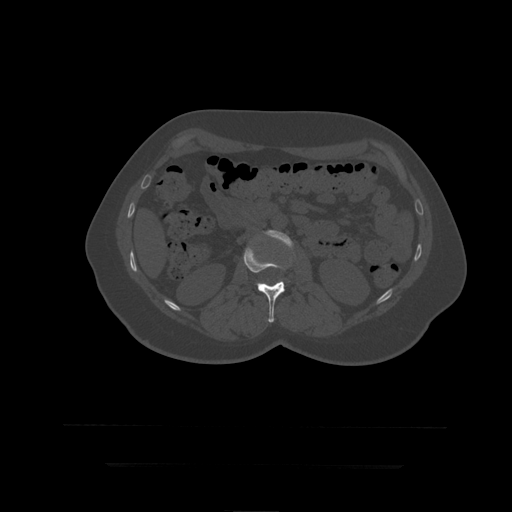
CT including the spine, one axial slice. Position 142 of 399 along the scan axis. Reconstruction kernel STANDARD. 120 kVp. Bone window (W 1800 / L 400 HU). 1.25 mm slice thickness. 512 × 512 image matrix. Patient age 41 years. Case-level facts recorded for this patient, not image findings: primary cancer: breast.
Outlined on this slice (semi-automatic segmentation, software-assisted and operator-edited):
- L2 vertebra: box from (x=244, y=247) to (x=285, y=323) px
- L3 vertebra: (x=263, y=230)–(x=294, y=248)